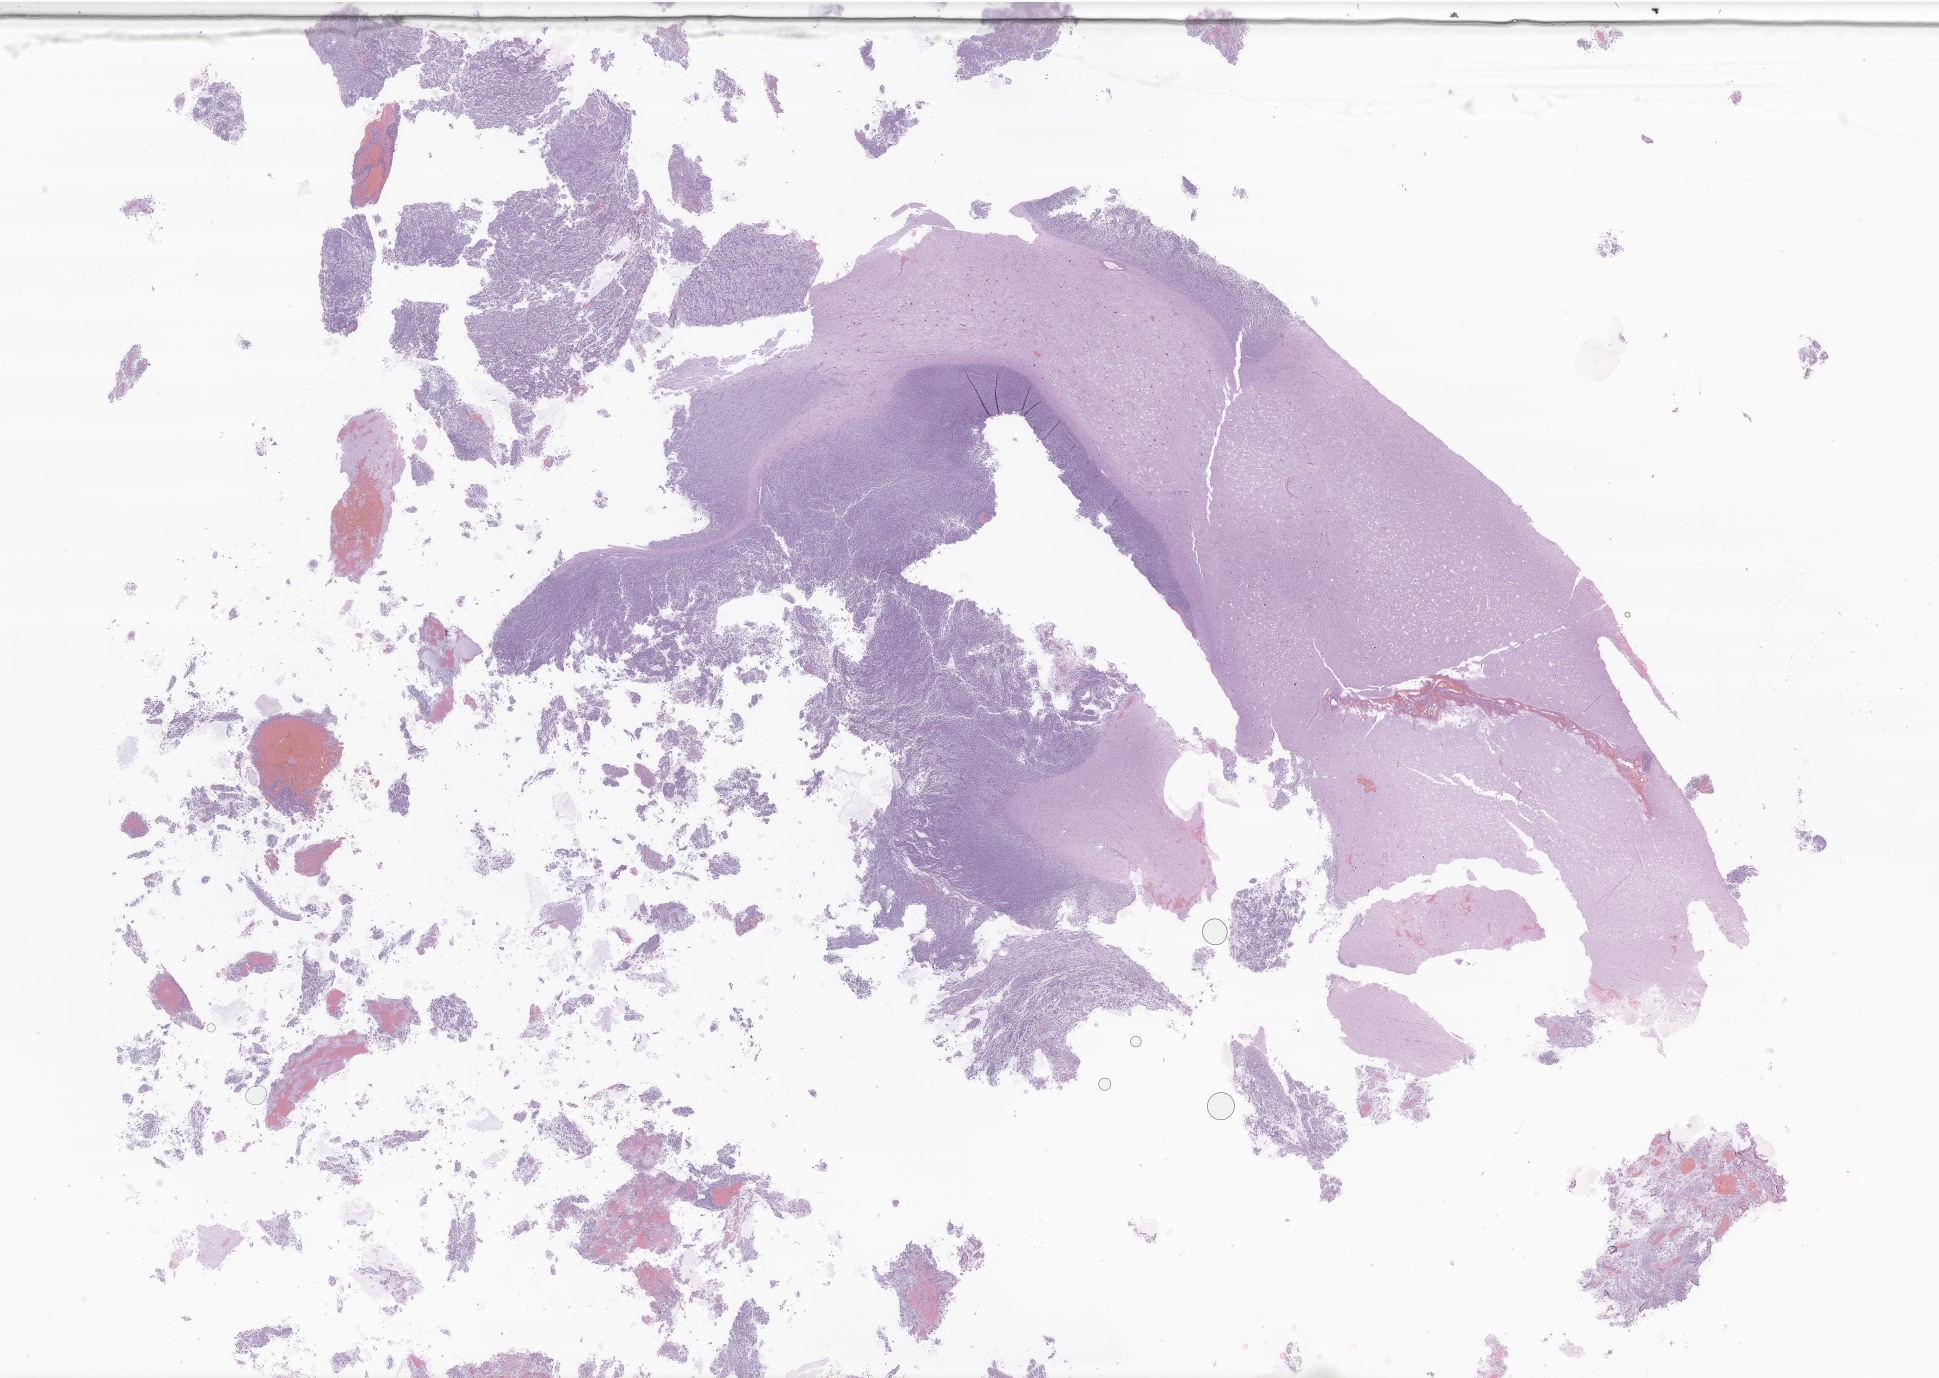
Digitized H&E-stained section of tumor tissue from the brain, whole scanned area (about 32.7 x 23.2 mm) shown as a low-resolution overview. FFPE section. Patient male; age 477 days.
• diagnosis: Neoplasm, malignant